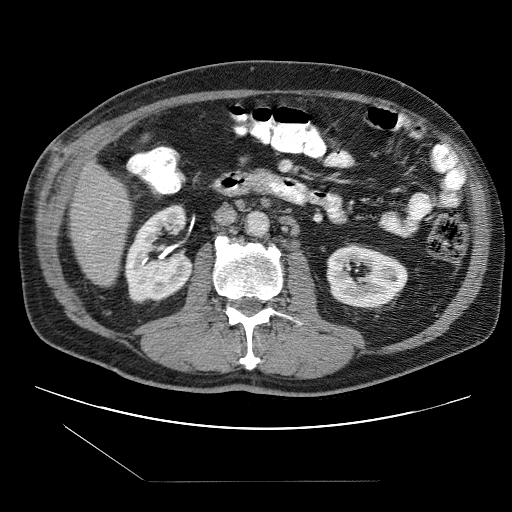
Contrast-enhanced abdominal CT (liver protocol), one axial slice; reconstruction kernel STANDARD; one of 2 acquisitions stored at this slice position; soft-tissue window (W 400 / L 40 HU); 2.5 mm slice thickness; 512 × 512 image matrix, field of view 400 × 400 mm. Case-level facts recorded for this patient, not image findings: diagnosis: hepatocellular carcinoma (patient treated with transarterial chemoembolisation; whether this scan precedes or follows treatment is not stated here); TNM stage (as recorded): Stage-IIIB; Child-Pugh class: A; tumour differentiation: well differentiated; tumour nodularity: multinodular.
Outlined on this slice (semi-automatically segmented with operator editing):
- liver parenchyma outside the tumour (the mass and vessels are separate outlines, so this box may not span the whole liver): bounding box <70,161,131,284> (left, top, right, bottom; pixels)